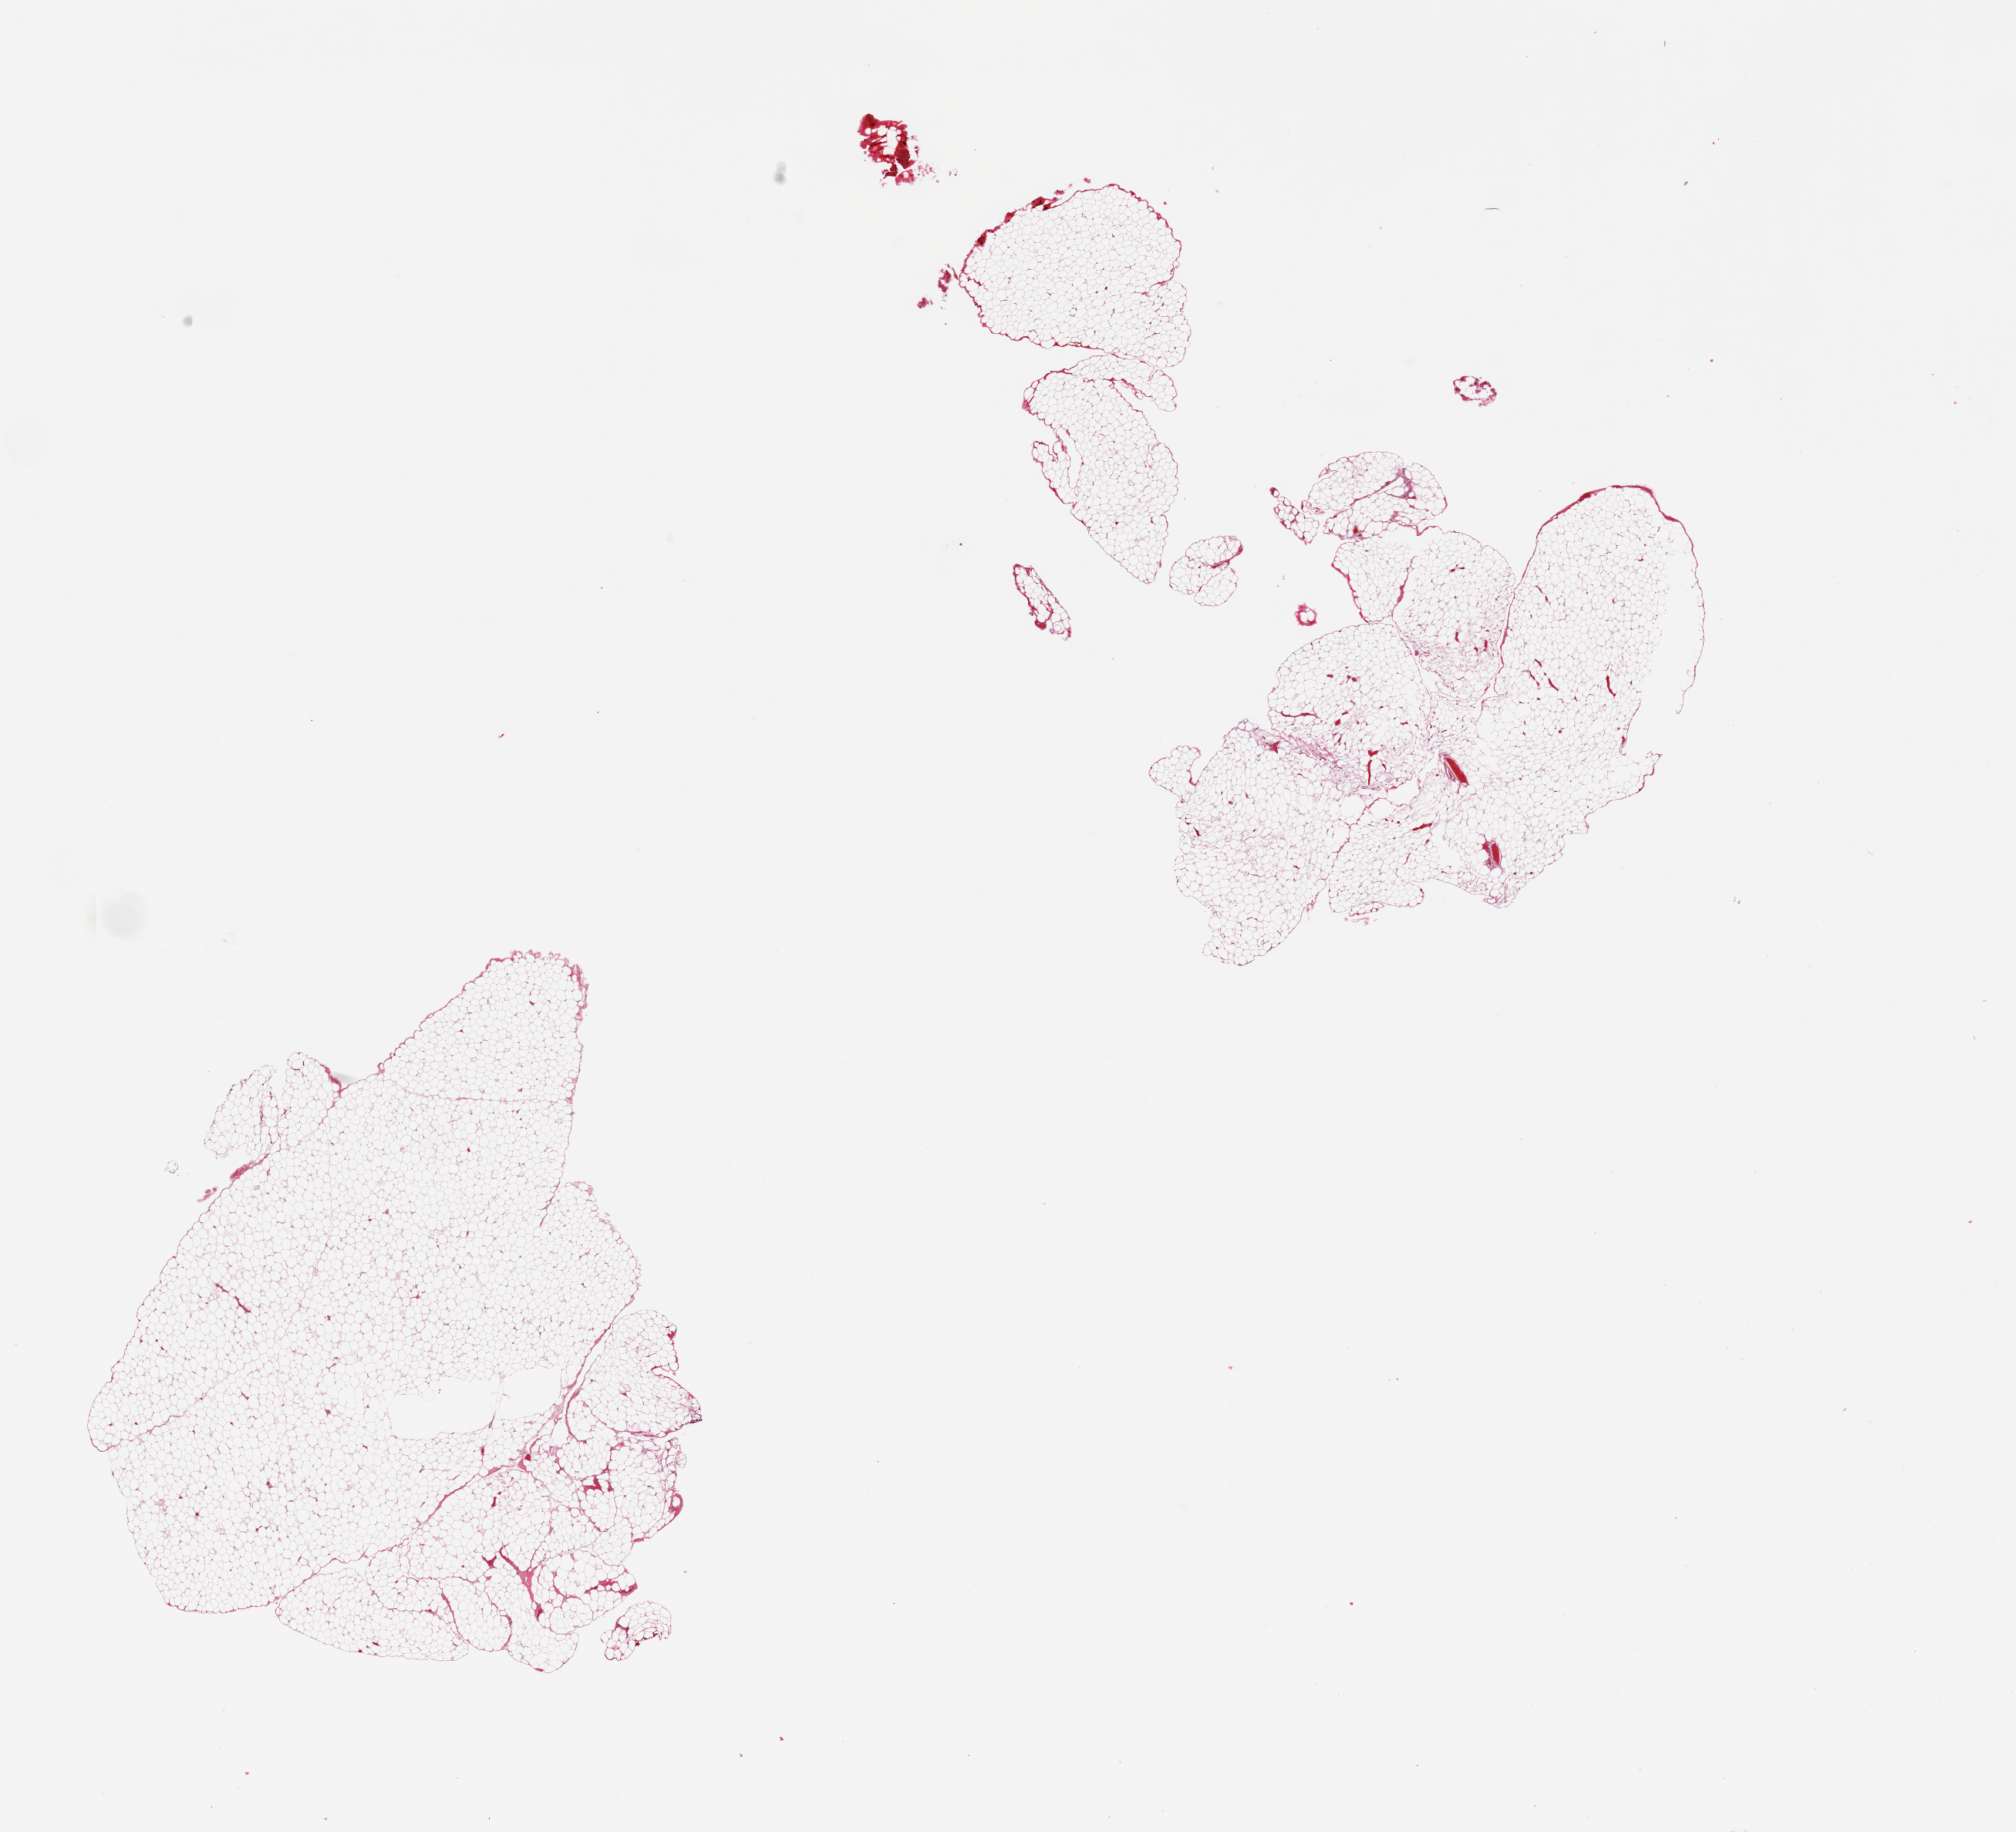
Digitized hematoxylin and eosin (H&E)-stained section — whole scanned area (about 20.7 x 18.8 mm) shown as a low-resolution overview. PAXgene-fixed paraffin-embedded (PFPE) section. Target tissue: omentum. Donor tissue sample. Donor: female.
Reviewer comment on this tissue sample: 2 pieces.